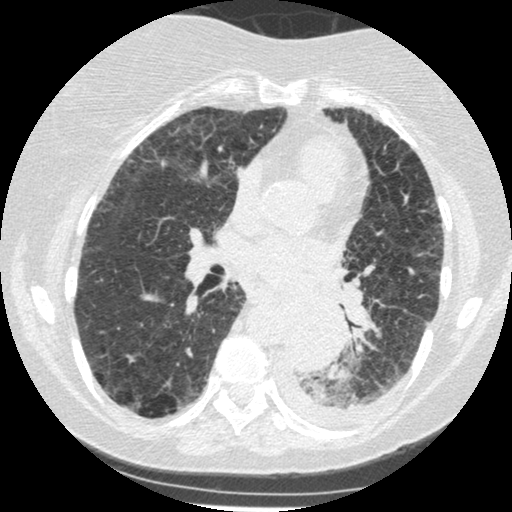
Low-dose screening chest CT, axial slice, third screening round (two years after baseline), lung window (W 1500 / L -600 HU), 1.25 mm slice thickness, standard (soft-tissue) reconstruction kernel (STANDARD), 120 kVp, slice 219 of 341 in the series, 512 × 512 image matrix. Female, age 60 years at enrolment.
- Expert-annotated lung lesion, bounding box [x1, y1, x2, y2] px = [273, 305, 342, 375].
- Reader record for this screening exam (exam-level; its link to the box is not recorded): non-calcified nodule or mass ≥4 mm, left lower lobe, 54 × 38 mm, smooth margins, soft tissue attenuation, pre-existing on the prior screen: yes; interval growth: yes.
- Later outcome: lung cancer diagnosed 15 days after this screen — small cell carcinoma, NOS, left lower lobe, undifferentiated (G4), stage IV (AJCC 6th edition), 69 mm at pathology.